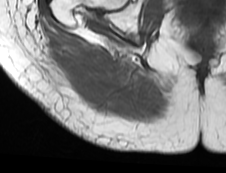
MRI of an extremity soft-tissue mass, one axial slice. Slice 24 of 73 in the series (ordered by position). MR volume resampled by the dataset authors to the PET/CT grid (not the native acquisition matrix). 3.27 mm slice thickness. 226 × 173 image matrix, field of view 221 × 169 mm. Female patient. Case-level facts recorded for this patient, not image findings: histological type: spindle cell suggestive of myxofibrosarcoma; grade: intermediate; site of the primary tumour: right buttock.
Outlined on this slice (expert contour drawn on MRI and transferred to this co-registered scan by the dataset authors):
- gross tumour volume (mass): bounding box [x1, y1, x2, y2] px = [47, 42, 119, 100]